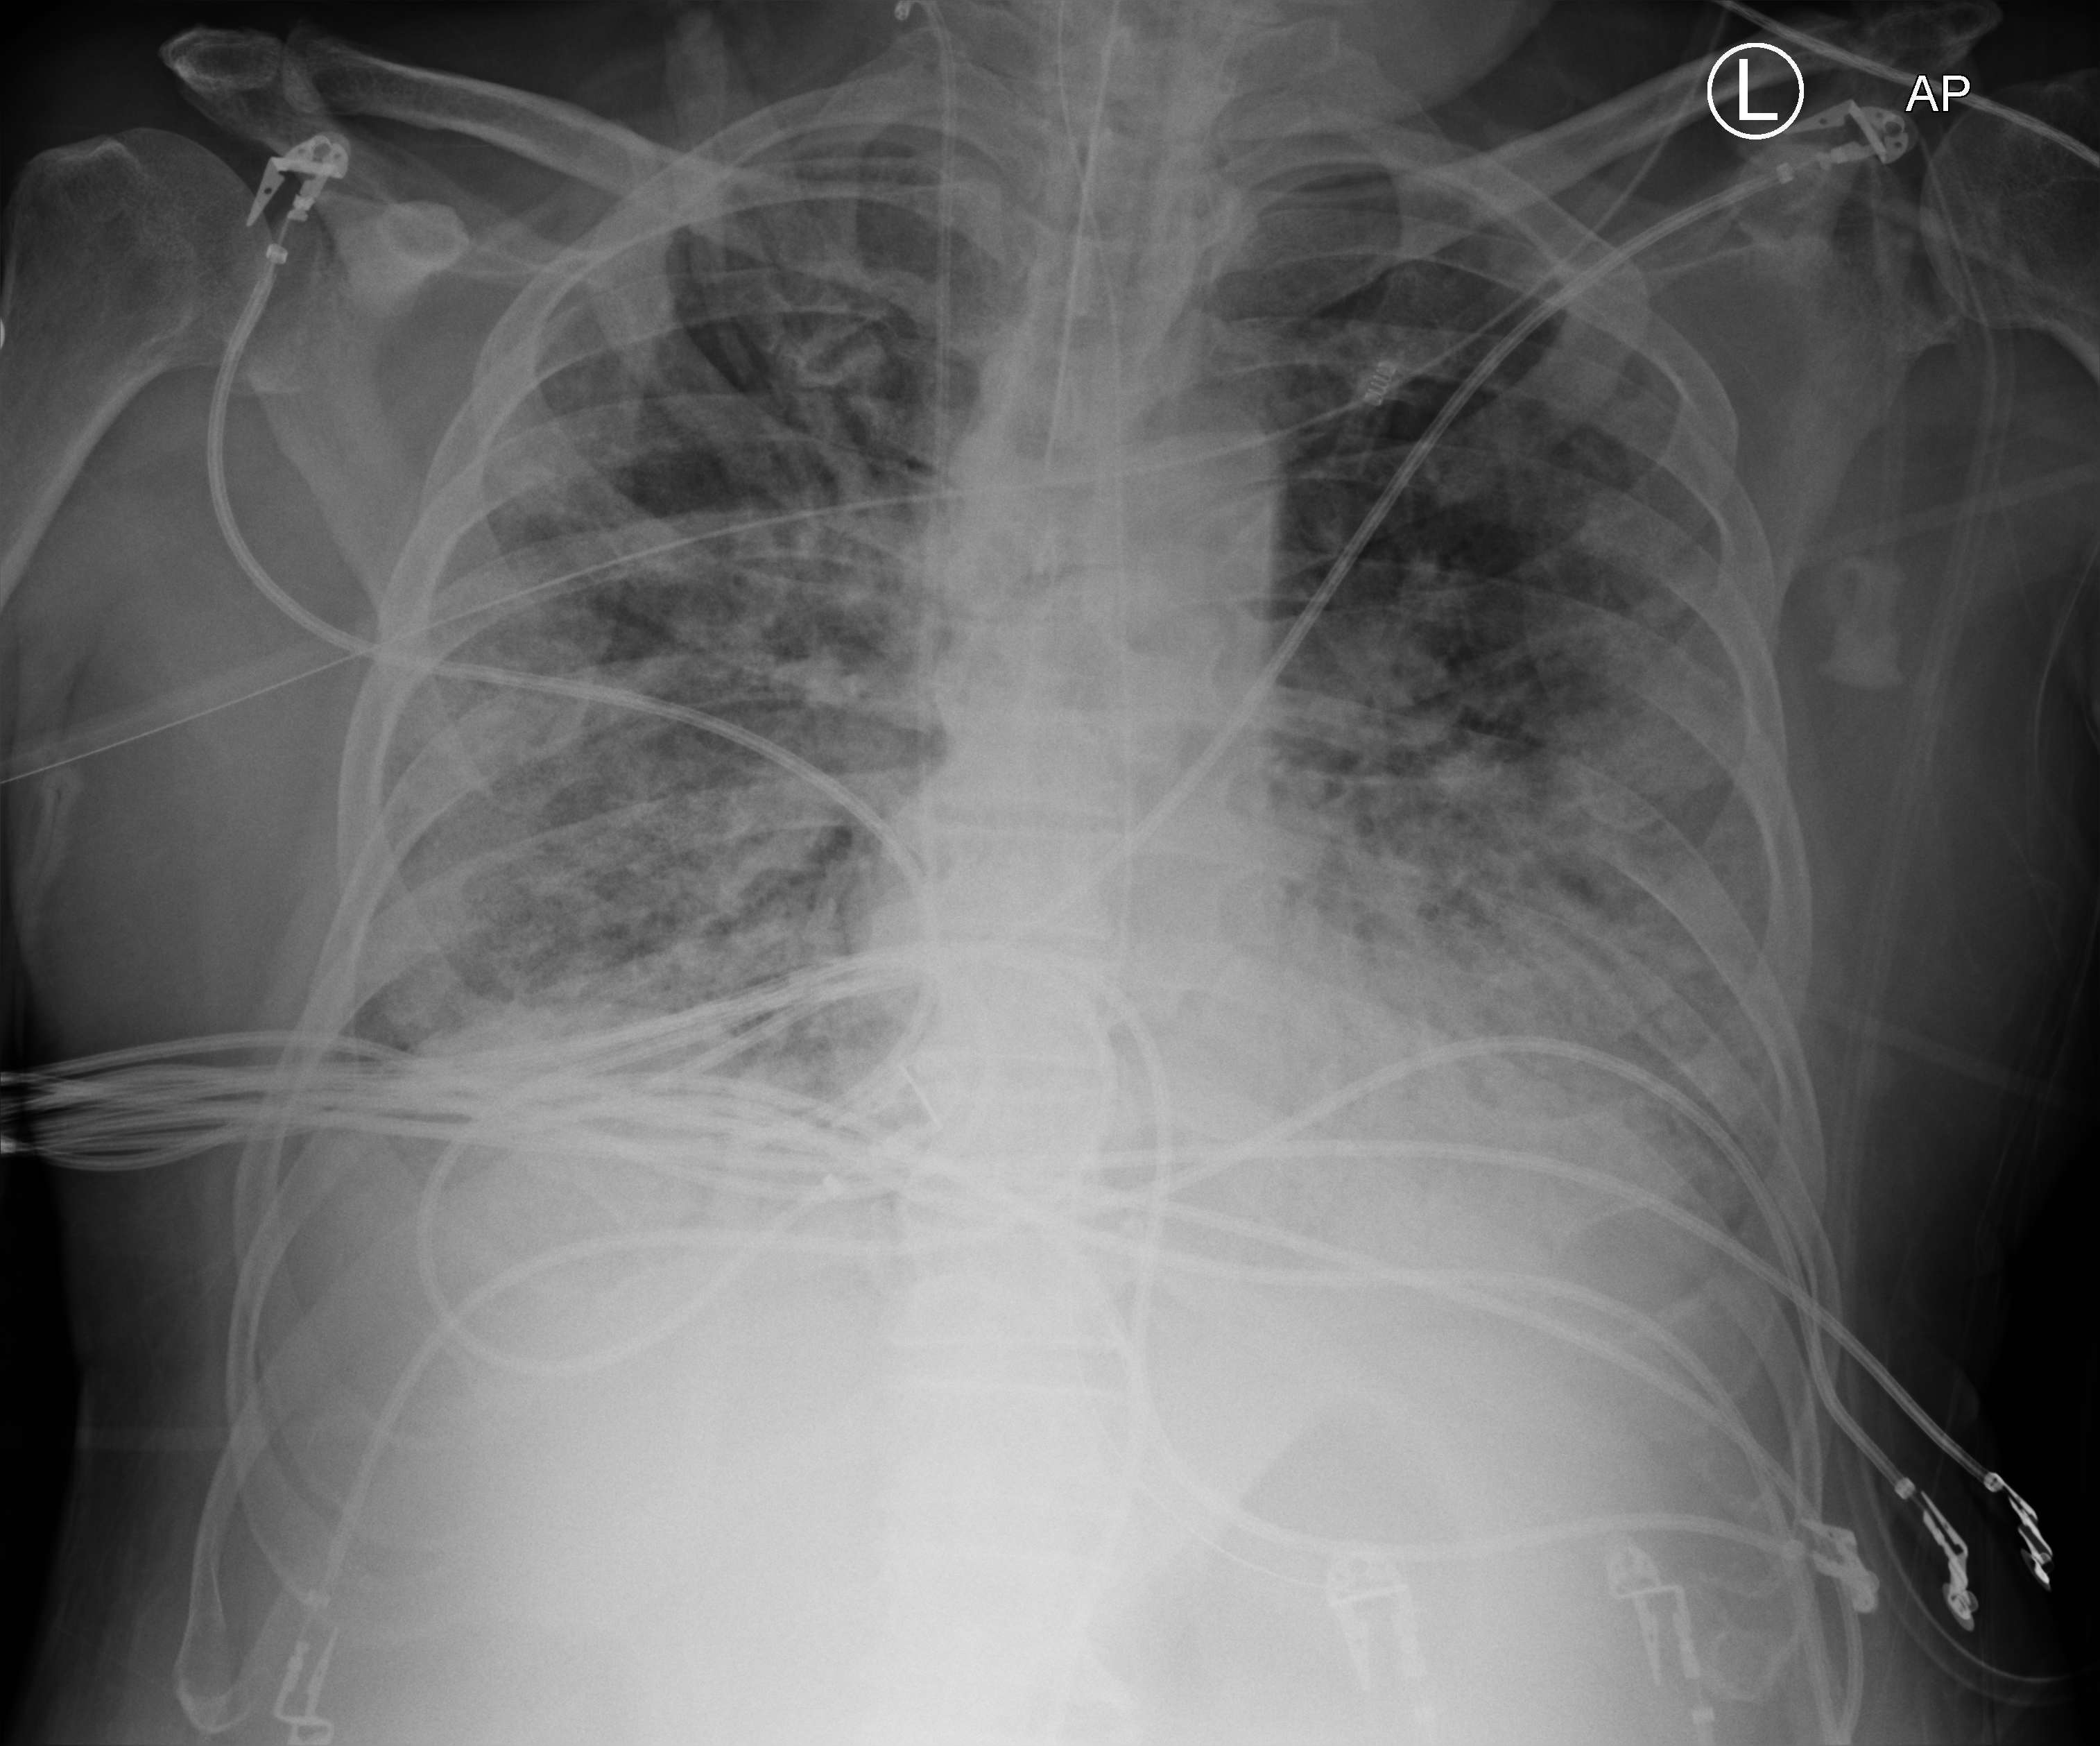
Portable chest radiograph; anteroposterior (AP) projection. Patient hospitalised with COVID-19; male, aged 75–90 years.
Admission-level facts for this patient (not findings on this image; timing relative to this image not recorded):
- mechanically ventilated during this hospital stay: yes
- diabetes (admission record): no